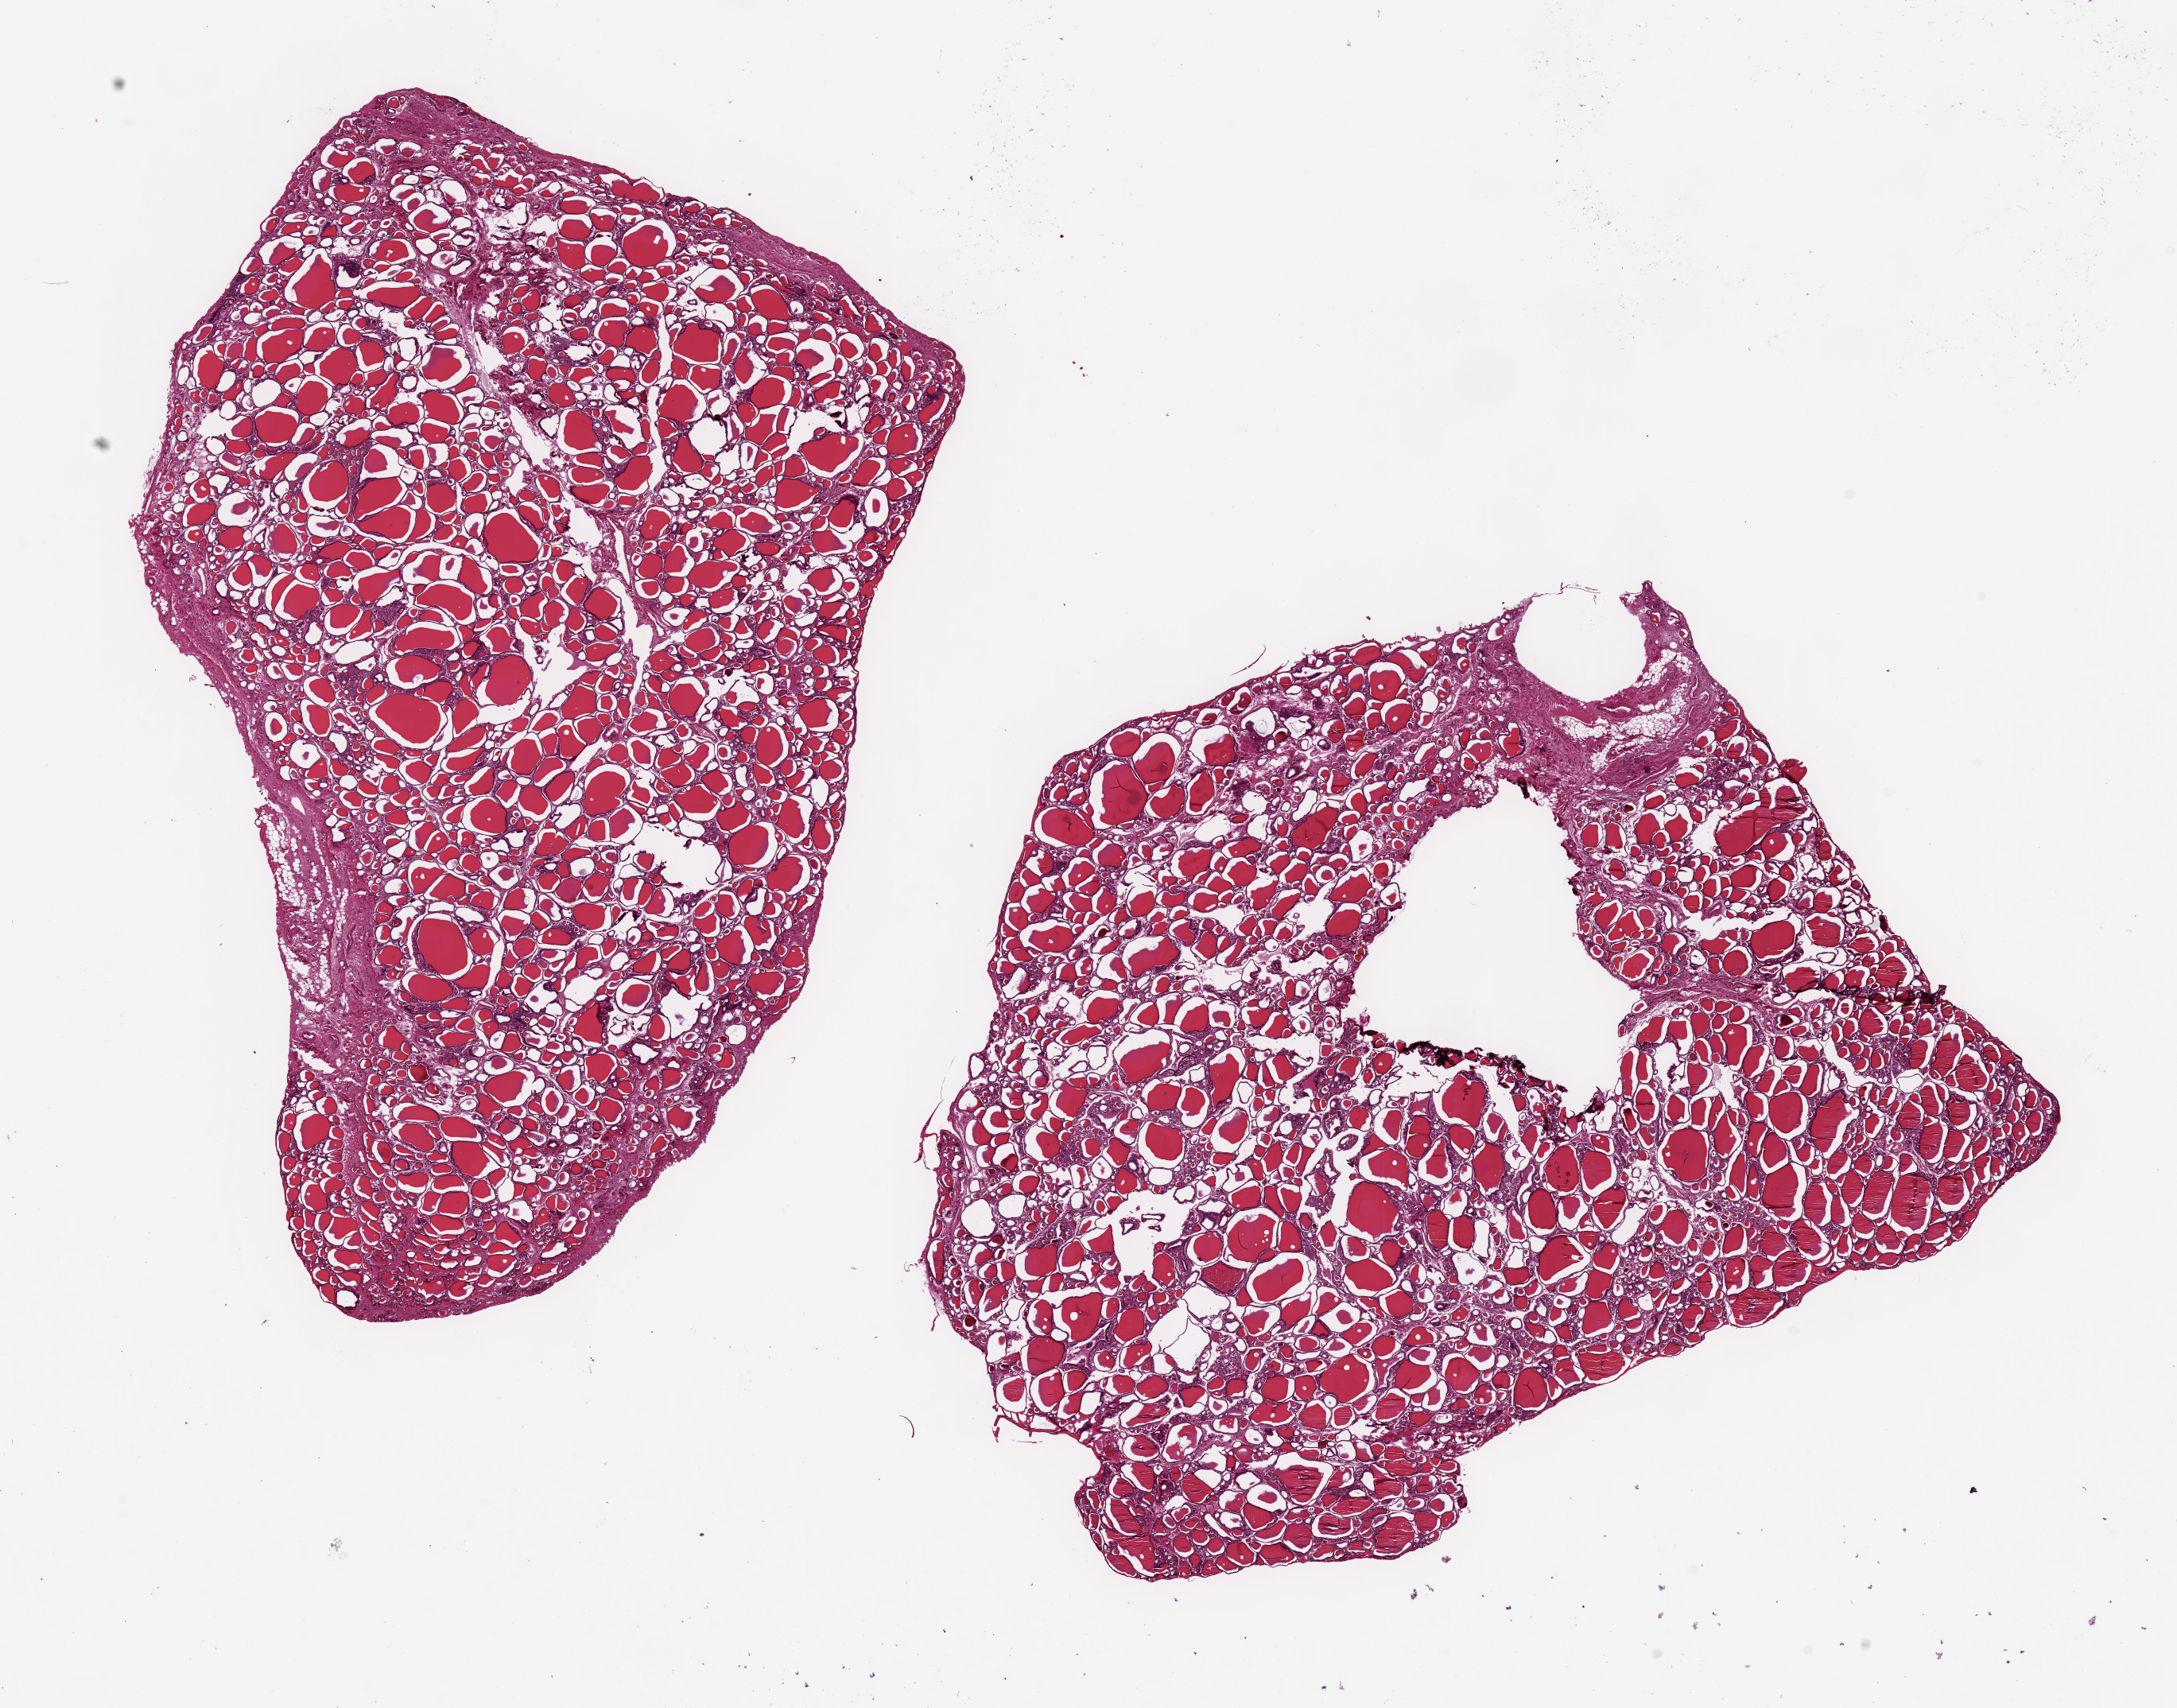
Haematoxylin and eosin whole-slide image, brightfield — shown as a low-resolution overview of the whole scanned area (about 21.7 x 17.0 mm, from a 20x scan). PAXgene-fixed, paraffin-embedded tissue. Target tissue: thyroid. Tissue donor sample. Male donor.
Reviewer comment on this tissue sample: 2 pieces 11x7 & 10x8mm; 1.3mm circular defect corresponds to cassette???s center-point.